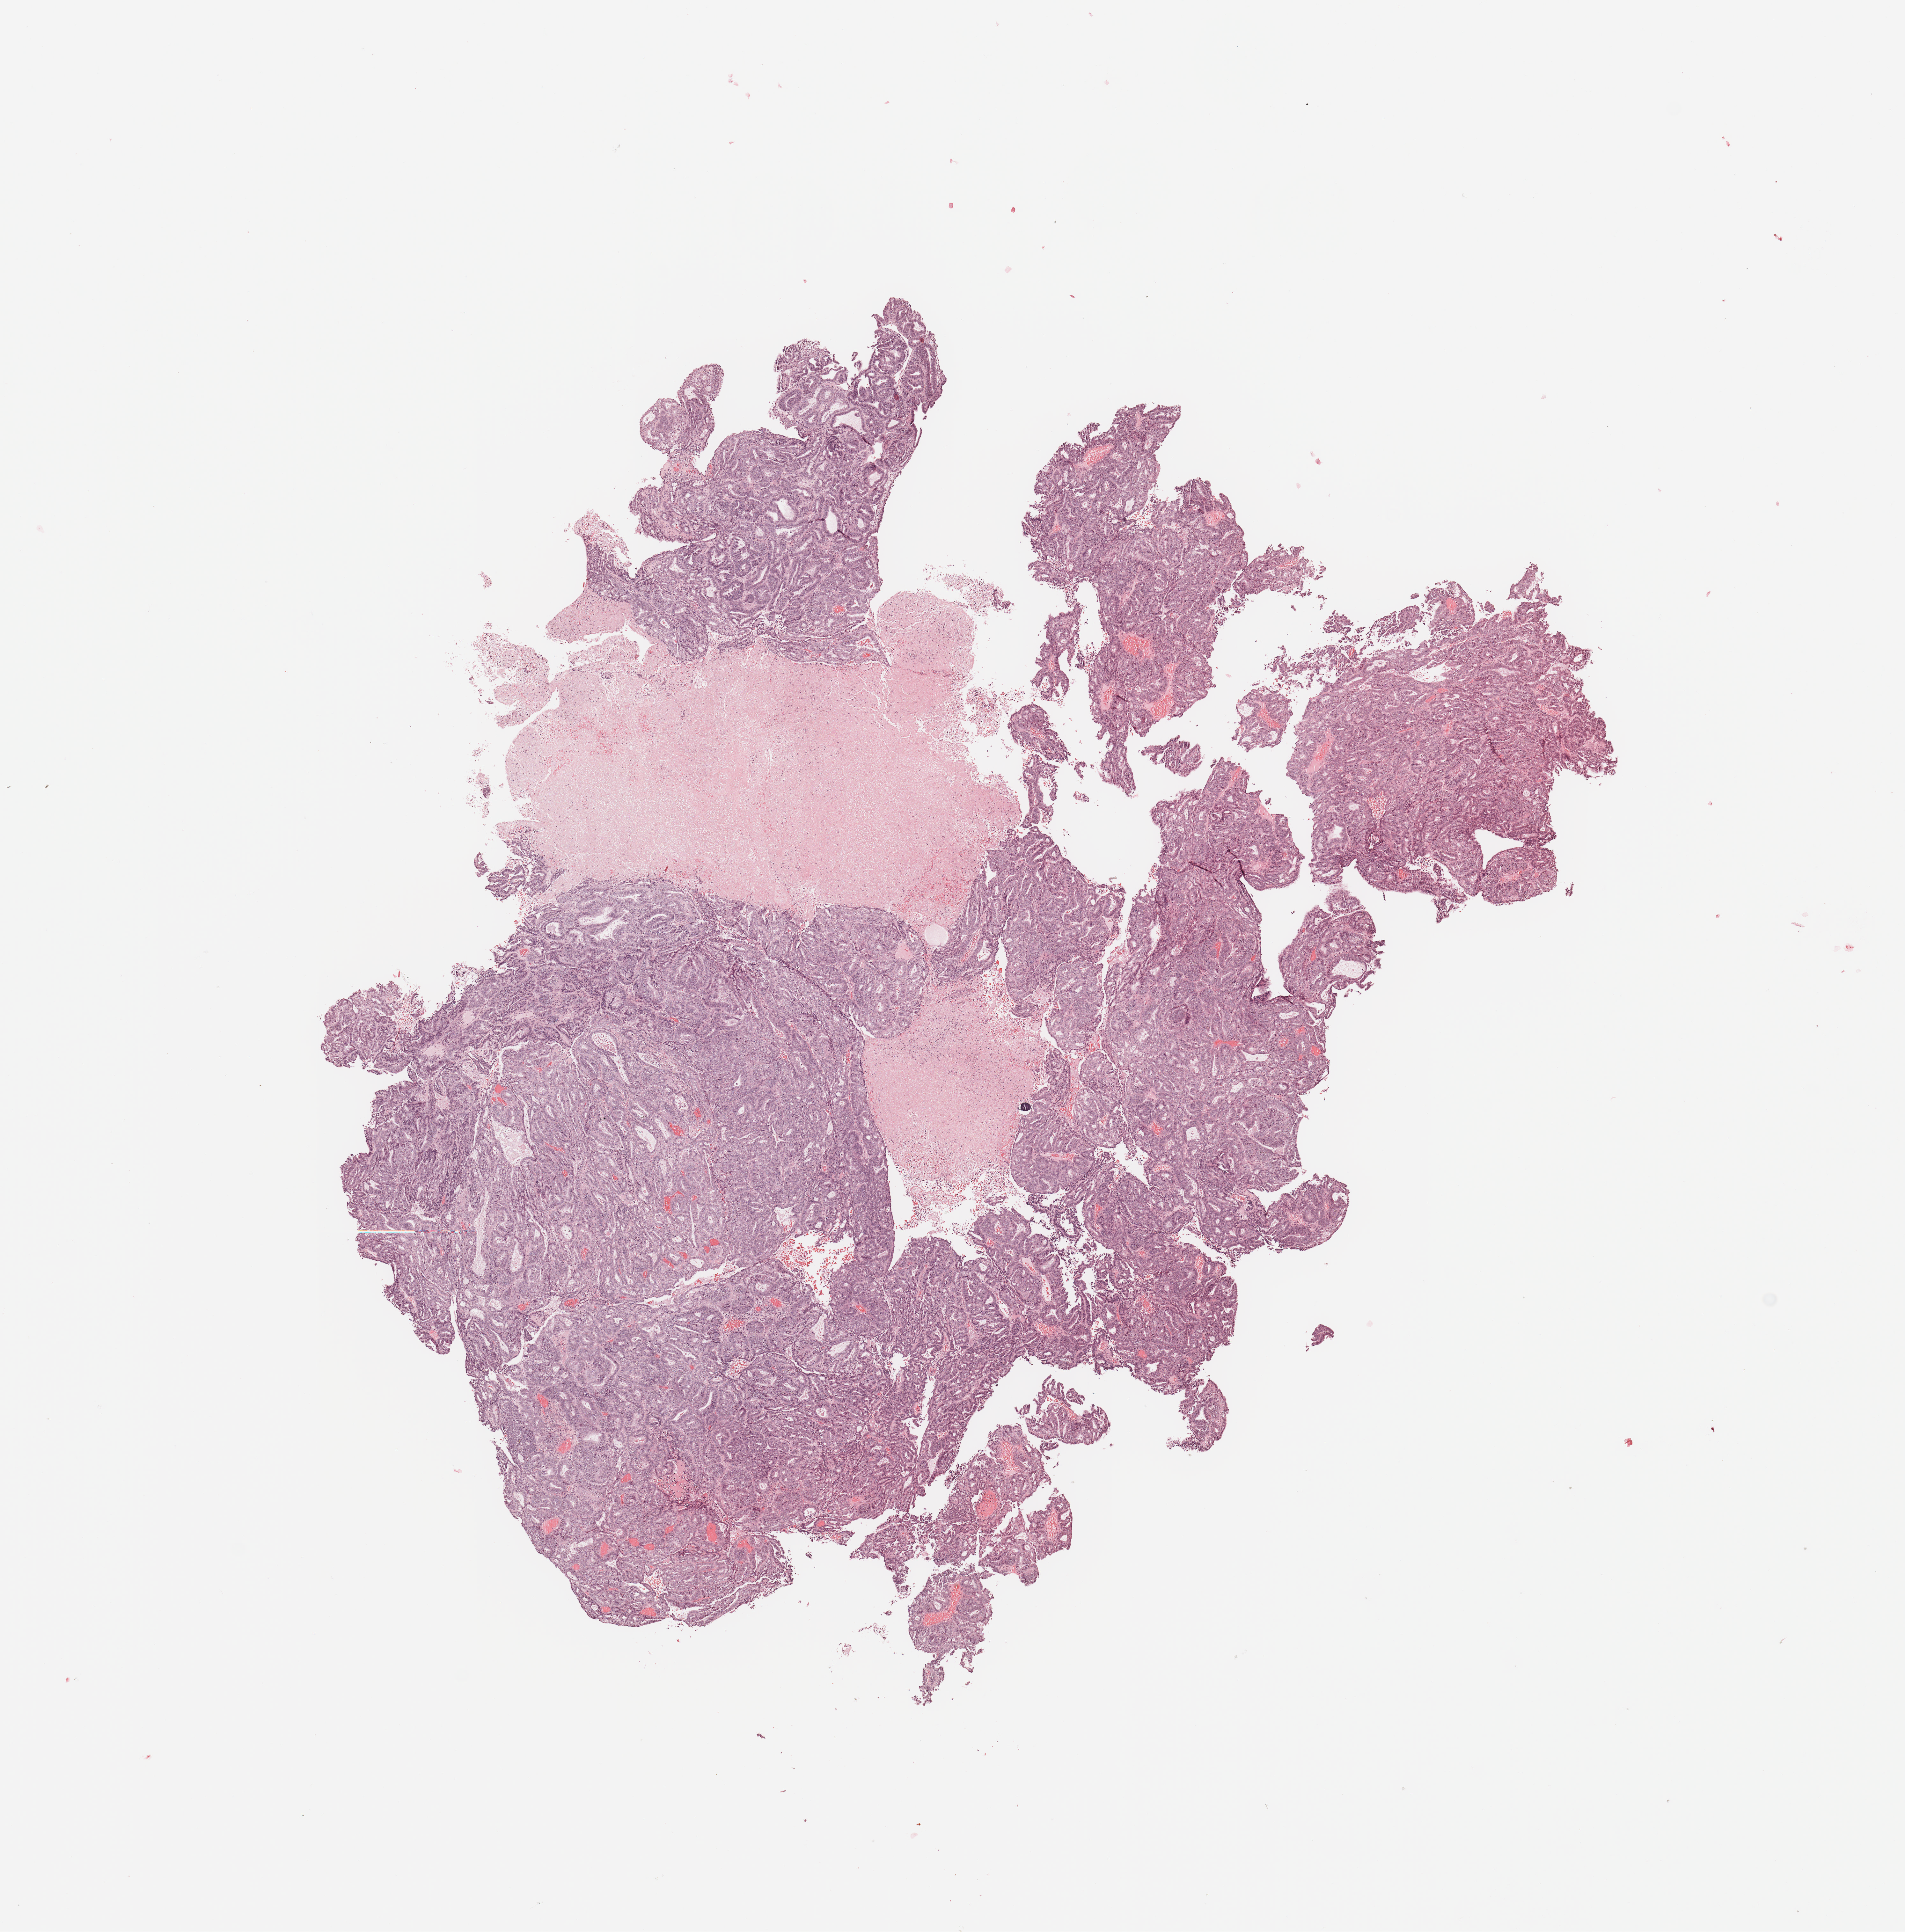
Hematoxylin and eosin (H&E) stained whole-slide image — whole scanned area (about 11.8 x 12.0 mm) shown as a low-resolution overview, tumour tissue sample, sampled site: uterus. Female, 72 y/o. Histologic grade: G1 (well differentiated). Pathologist review of this section (percent, as recorded): tumour nuclei 90%, necrosis 20%.
AJCC pathologic stage: I. Histologic diagnosis: Endometrioid adenocarcinoma, NOS.